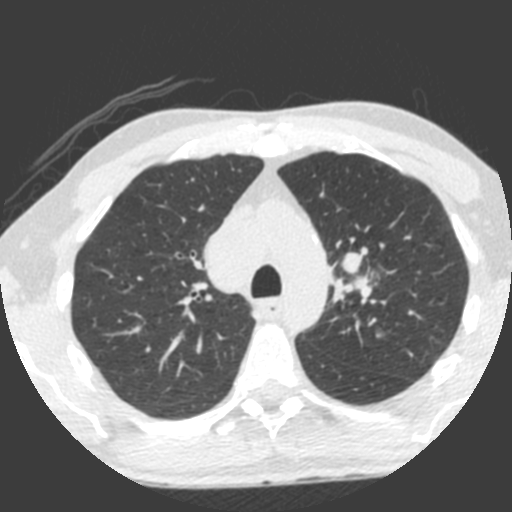
Chest CT (low-dose screening protocol), one axial image; third screening round (two years after baseline); lung window (W 1500 / L -600 HU); standard (soft-tissue) reconstruction kernel (B). Male participant, aged 55 years at enrolment.
- Expert reader's lesion annotation, bounding box [x1, y1, x2, y2] px = [308, 236, 387, 322].
- The exam's reader record, not a measurement of the box and not confirmed to be the same lesion: non-calcified nodule or mass ≥4 mm, left upper lobe, 49 × 29 mm, spiculated (stellate) margins, soft tissue attenuation, pre-existing on the prior screen: yes; interval growth: yes.
- Later outcome: lung cancer diagnosed 0 days after this screen — small cell carcinoma, NOS, left upper lobe, undifferentiated (G4), stage IV (AJCC 6th edition), 60 mm at pathology.